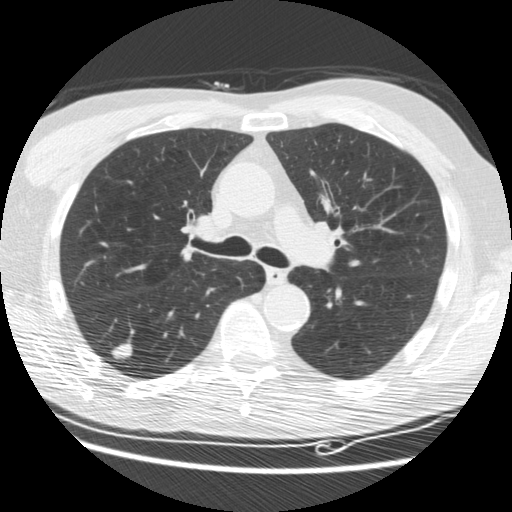
Chest CT (low-dose screening protocol), one axial image, third screening round (two years after baseline), lung window (W 1500 / L -600 HU), 2.5 mm slice thickness, standard (soft-tissue) reconstruction kernel (STANDARD), 120 kVp. Male, age 62 years at enrolment.
Expert-annotated lung lesion, bounding box <100,333,142,370> (left, top, right, bottom; pixels). The screening reader recorded 3 non-calcified nodules or masses ≥4 mm on this exam (right lower lobe, right lower lobe, right lower lobe); which of them this box marks is not recorded. Official screen result: positive, other. Participant outcome: lung cancer diagnosed 33 days after this screen — adenocarcinoma, NOS, right lower lobe, moderately differentiated (G2), stage IIIB (AJCC 6th edition), 15 mm at pathology.